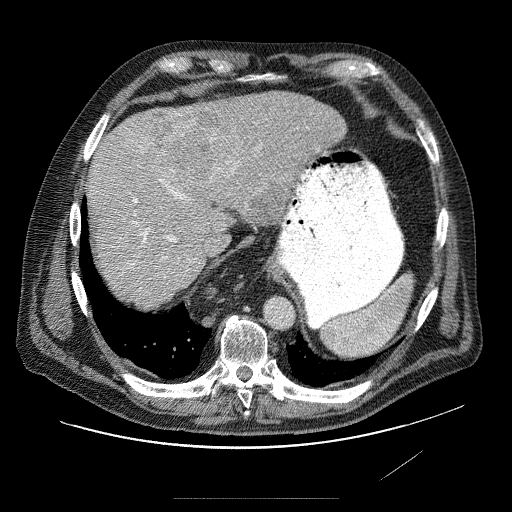
Contrast-enhanced abdominal CT (liver protocol), one axial slice. Soft-tissue window (W 400 / L 40 HU). 2.5 mm slice thickness. 512 × 512 image matrix, field of view 420 × 420 mm. Case-level facts recorded for this patient, not image findings: diagnosis: hepatocellular carcinoma (patient treated with transarterial chemoembolisation; whether this scan precedes or follows treatment is not stated here); TNM stage (as recorded): Stage-IVA.
Structures marked on this image (semi-automatic segmentation, software-assisted and operator-edited):
- liver parenchyma outside the tumour (the mass and vessels are separate outlines, so this box may not span the whole liver): bounding box (x1, y1, x2, y2) in pixels: (86, 92, 346, 290)
- mass: (128, 103, 297, 223)
- liver vessels: (102, 151, 321, 260)